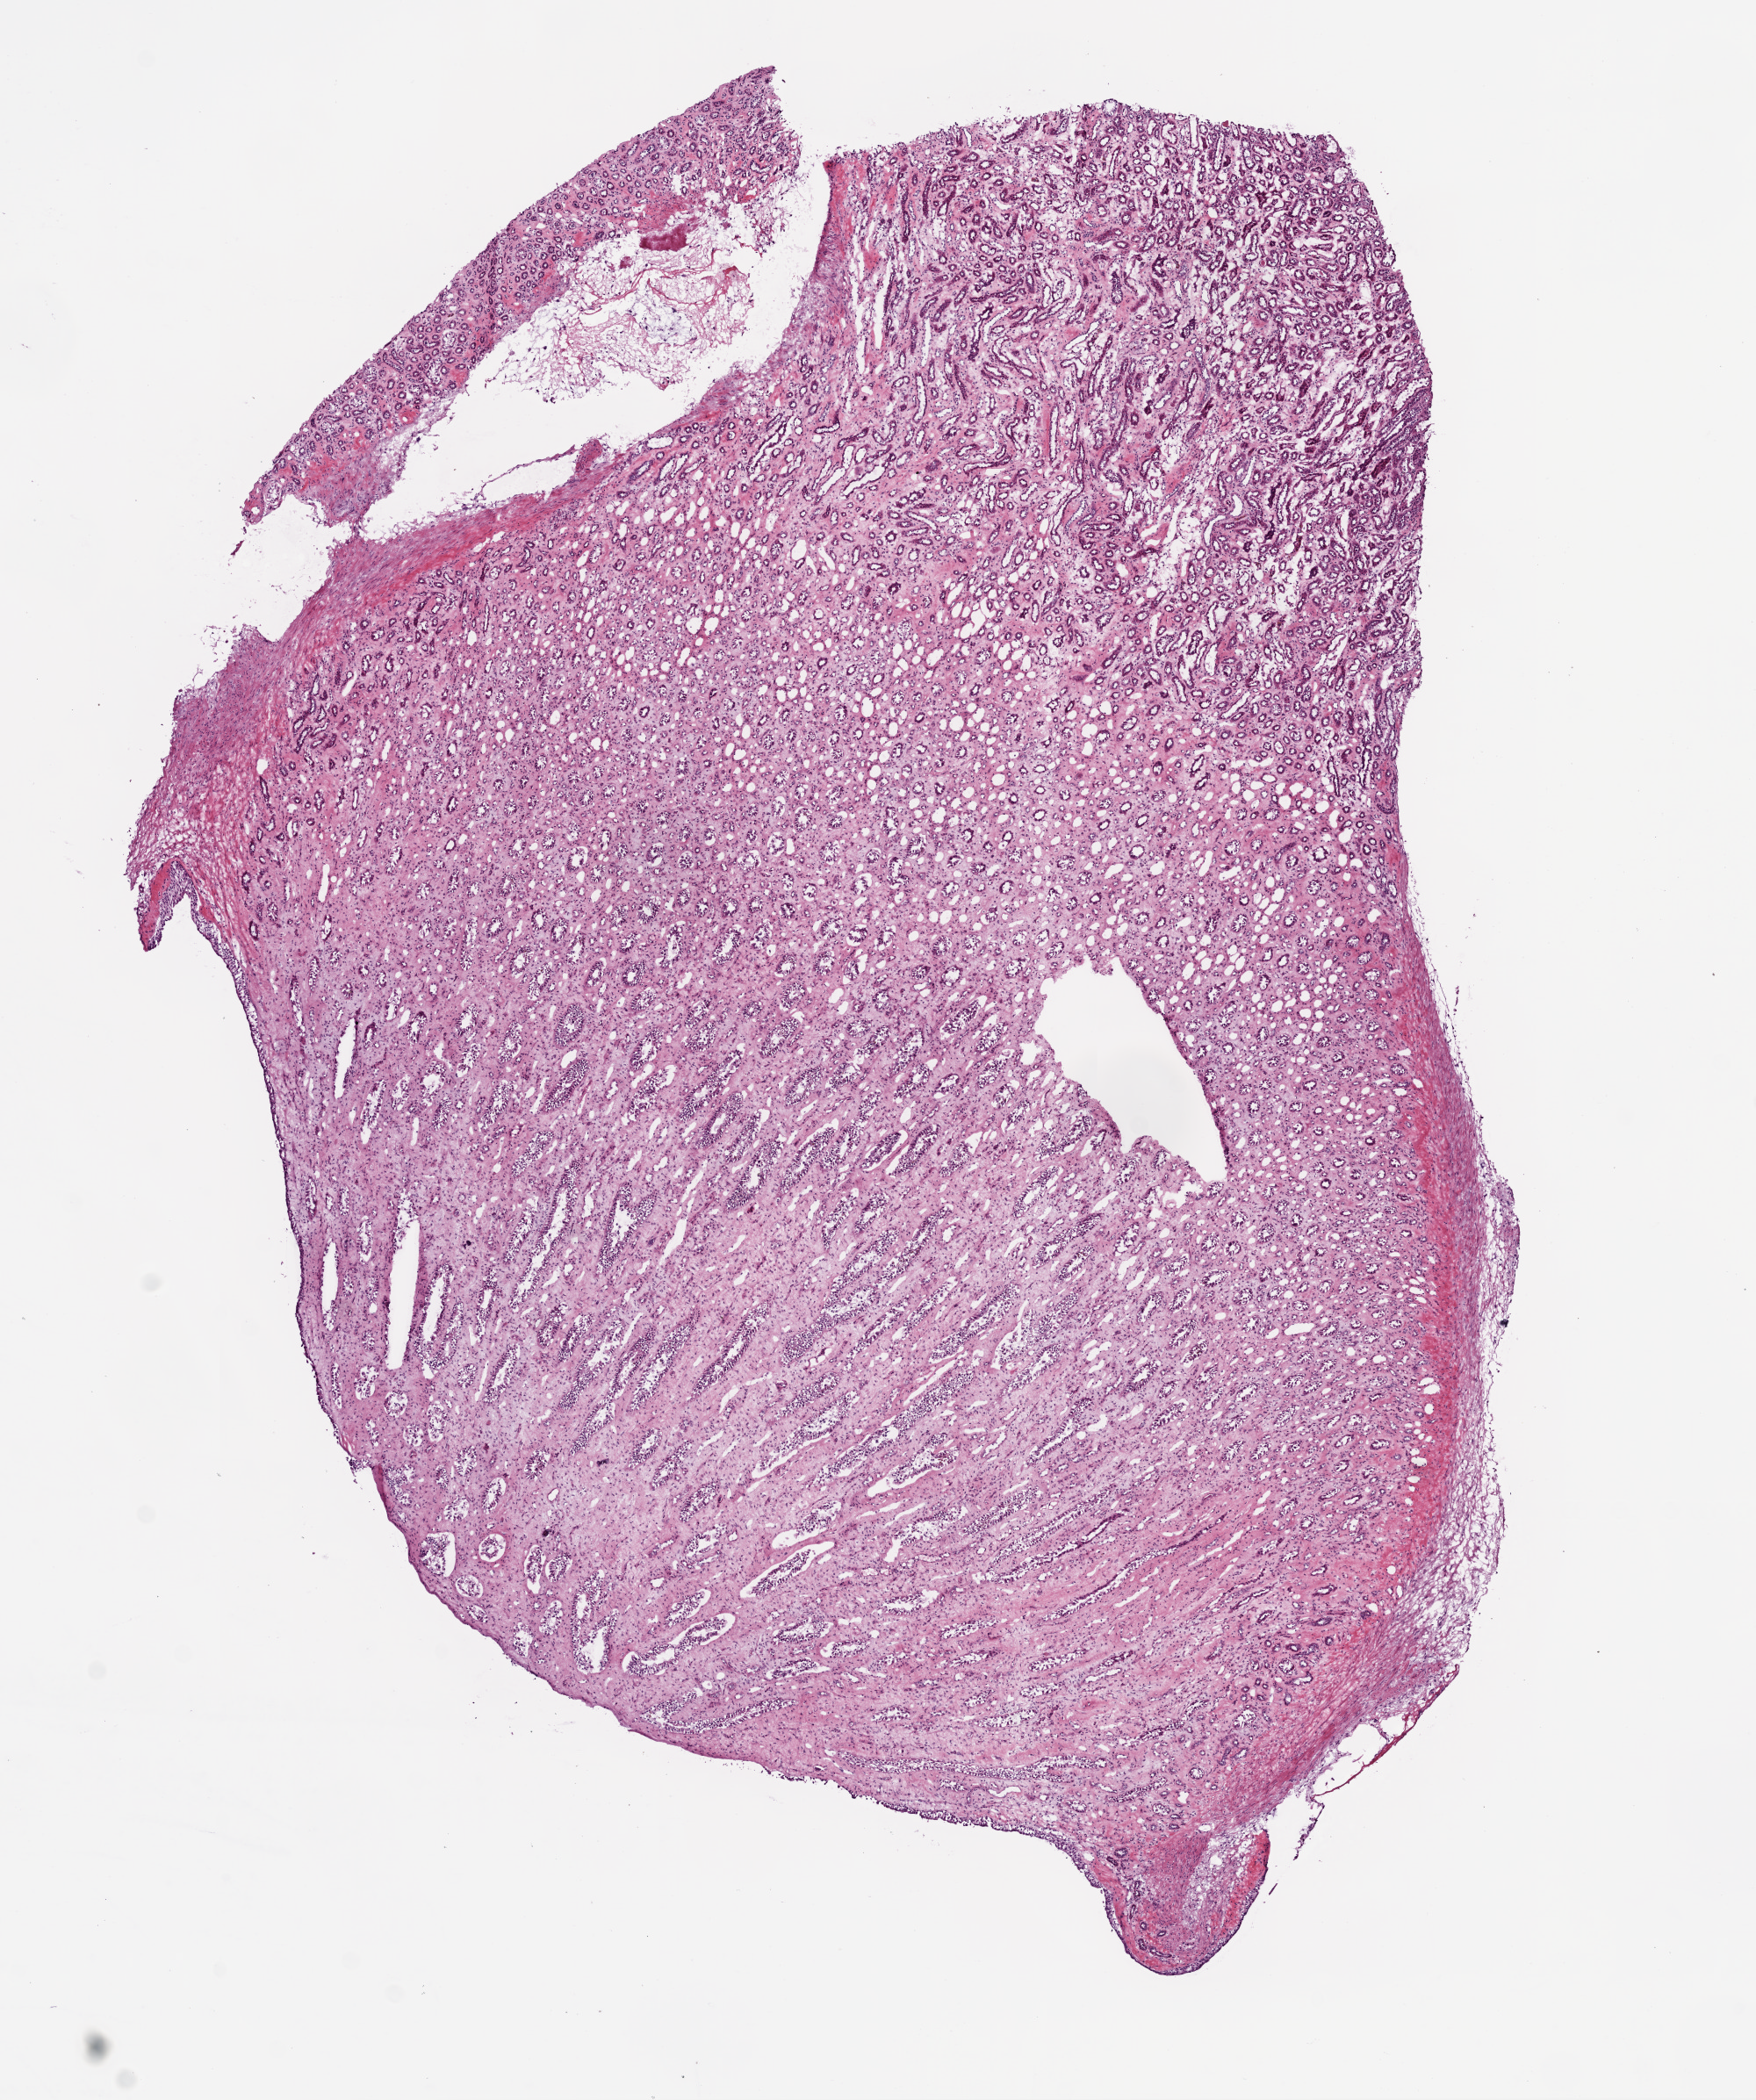
H&E whole-slide image, shown as a low-resolution overview of the whole scanned area (about 8.0 x 9.6 mm), frozen section from the bottom of the tissue portion, solid tissue normal (non-tumour tissue) sample from the kidney. Female, age 70 years at initial diagnosis.
This section: solid tissue normal sample (biorepository sample class). Patient diagnosis: Clear cell adenocarcinoma, NOS.